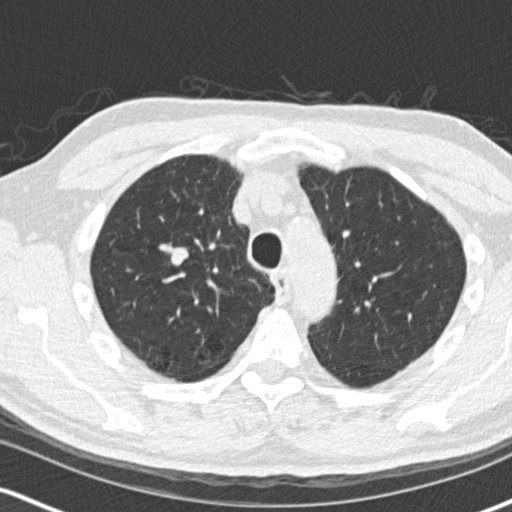
Low-dose screening chest CT, one axial slice. Position 118 of 170 along the scan axis. Reconstruction kernel B30f. 120 kVp. Lung window (W 1500 / L -600 HU). 512 × 512 image matrix, field of view 320 × 320 mm.
Annotated regions visible in this slice (outlined manually by an expert reader):
- lesion 1 (tumor, upper lobe of right lung): box from (x=171, y=247) to (x=189, y=266) px